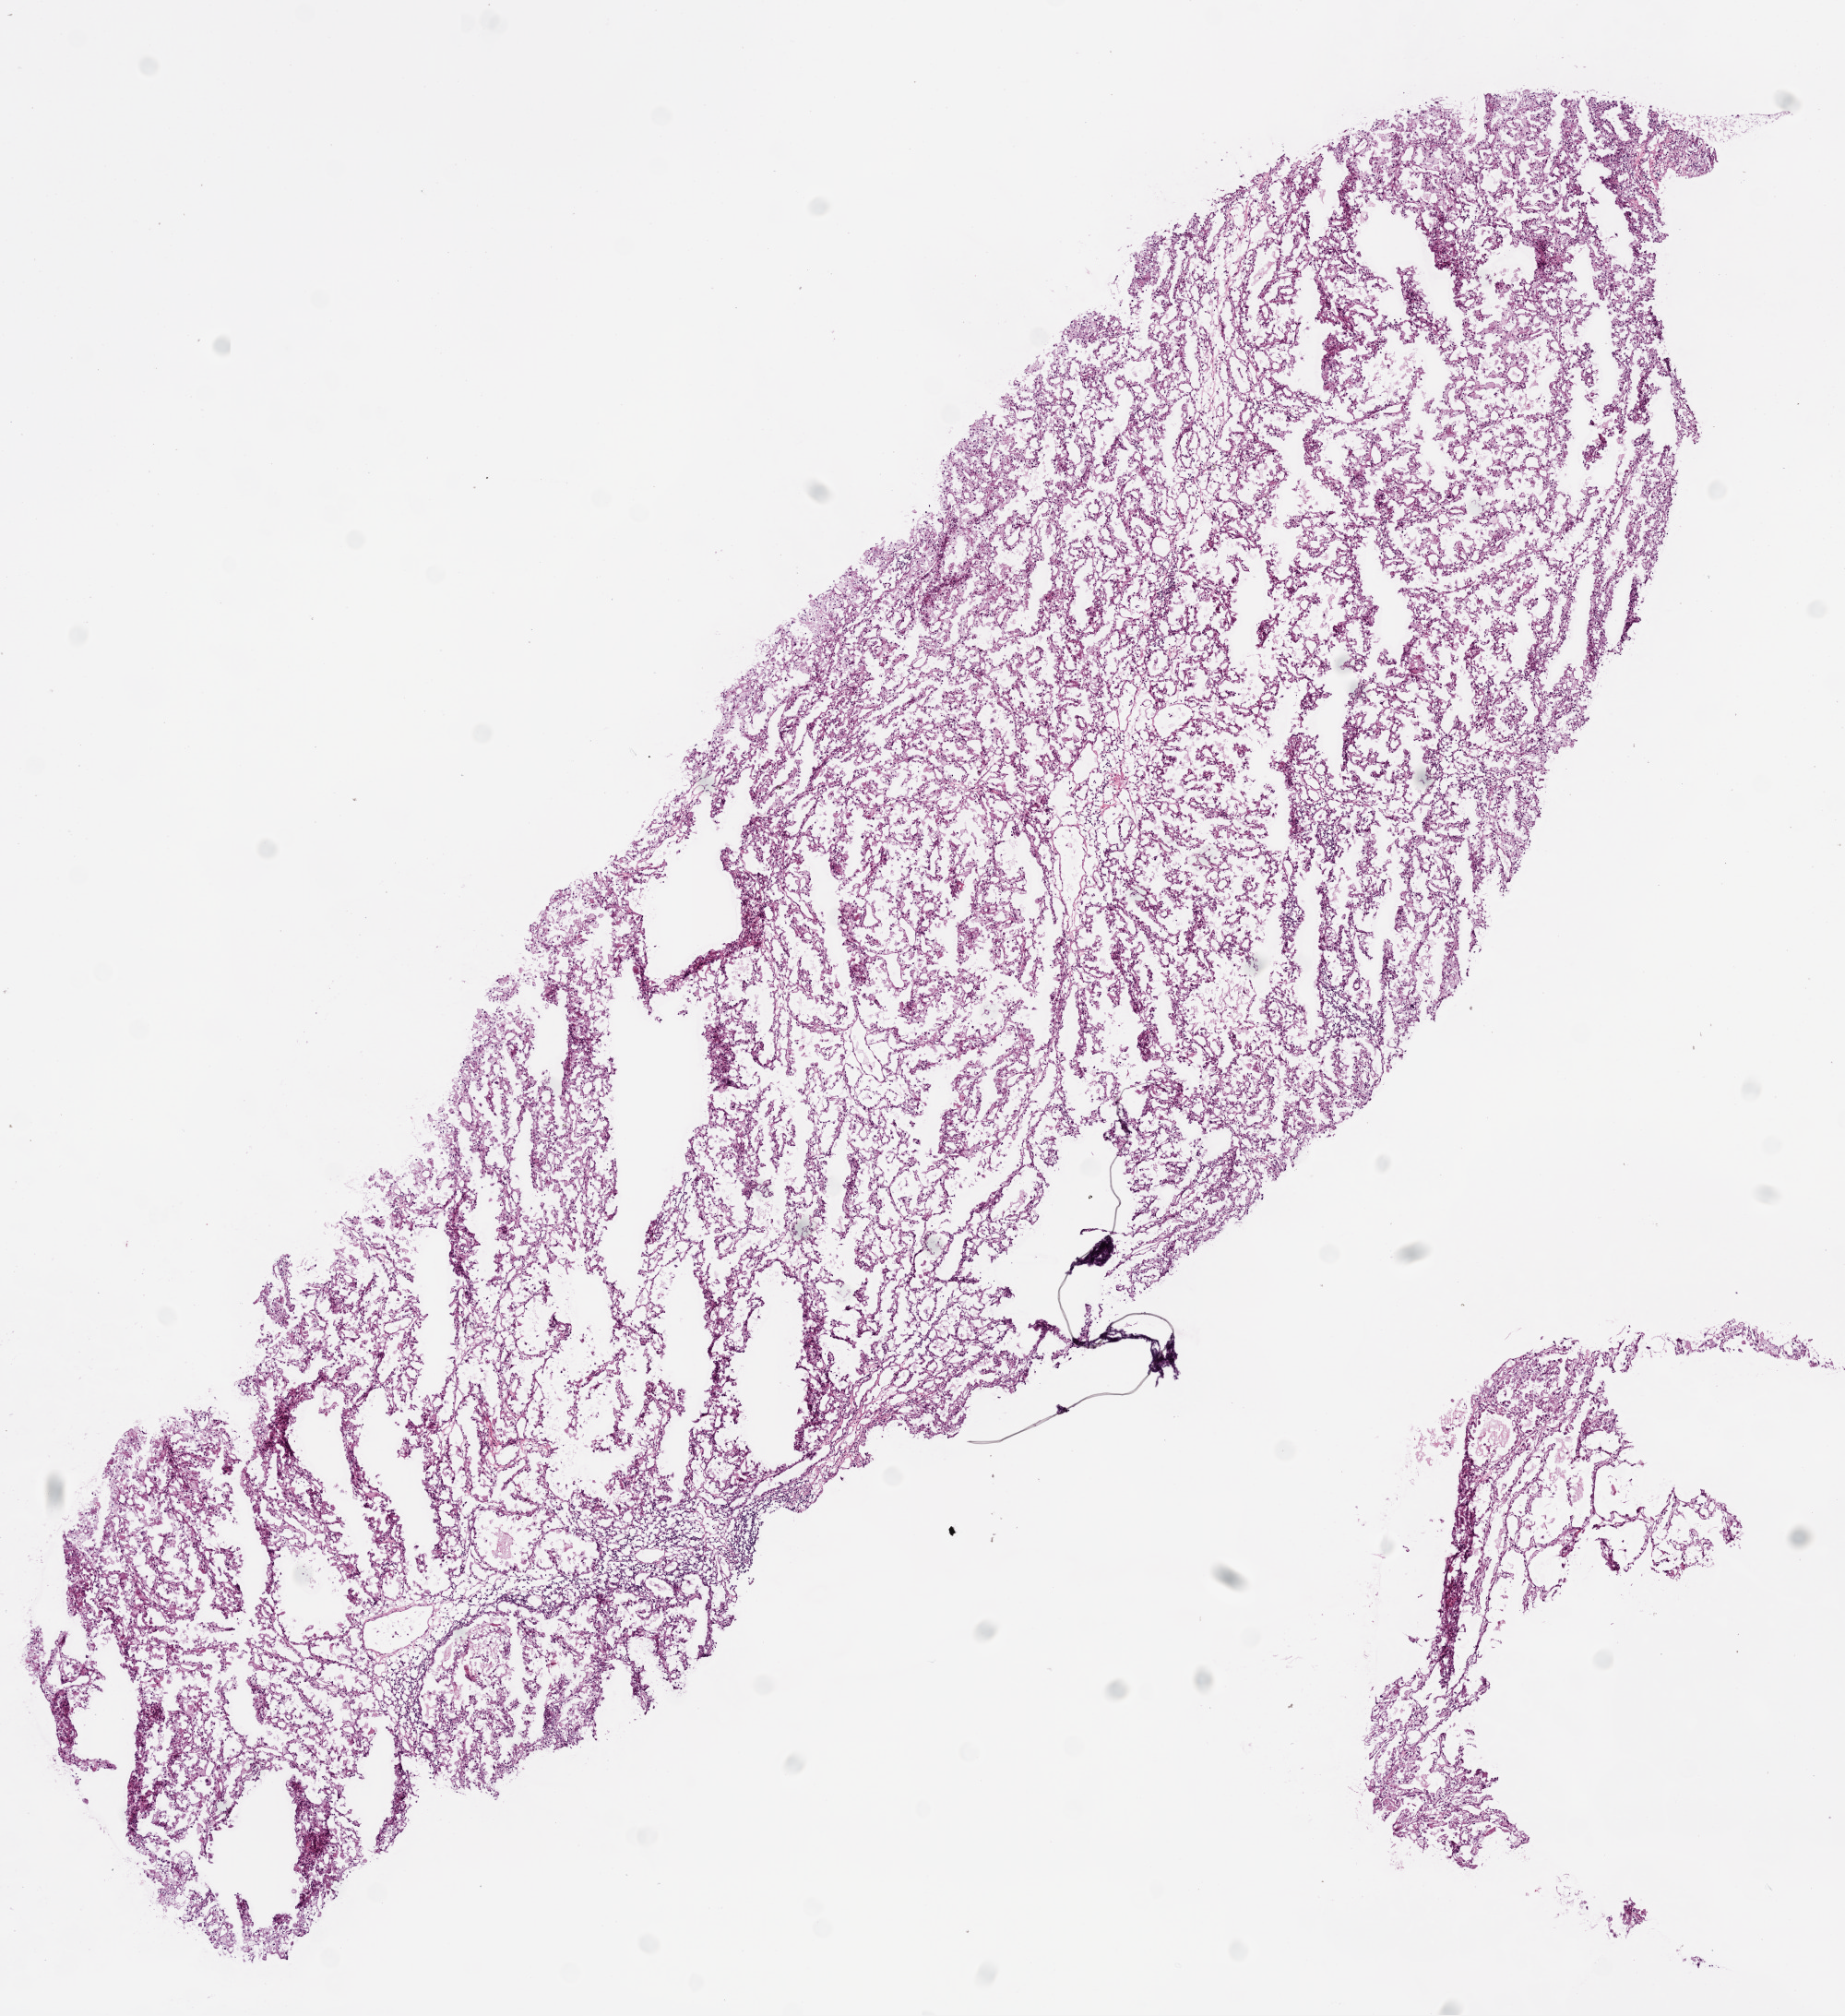
Digitized H&E tissue section (whole slide) — low-resolution overview of the scanned area, about 8.0 x 8.8 mm (from a 20x scan); frozen section from the bottom of the tissue portion; sample: primary tumour, kidney. Patient: male, age at initial diagnosis 46 years. Histologic grade: G3 (poorly differentiated). Pathologist review of this section (percent, as recorded): tumour cells 100%, tumour nuclei 90%, necrosis 0%. Infiltration values recorded for this section: lymphocyte infiltration 5%.
Histologic diagnosis: Clear cell adenocarcinoma, NOS. AJCC pathologic stage: I.